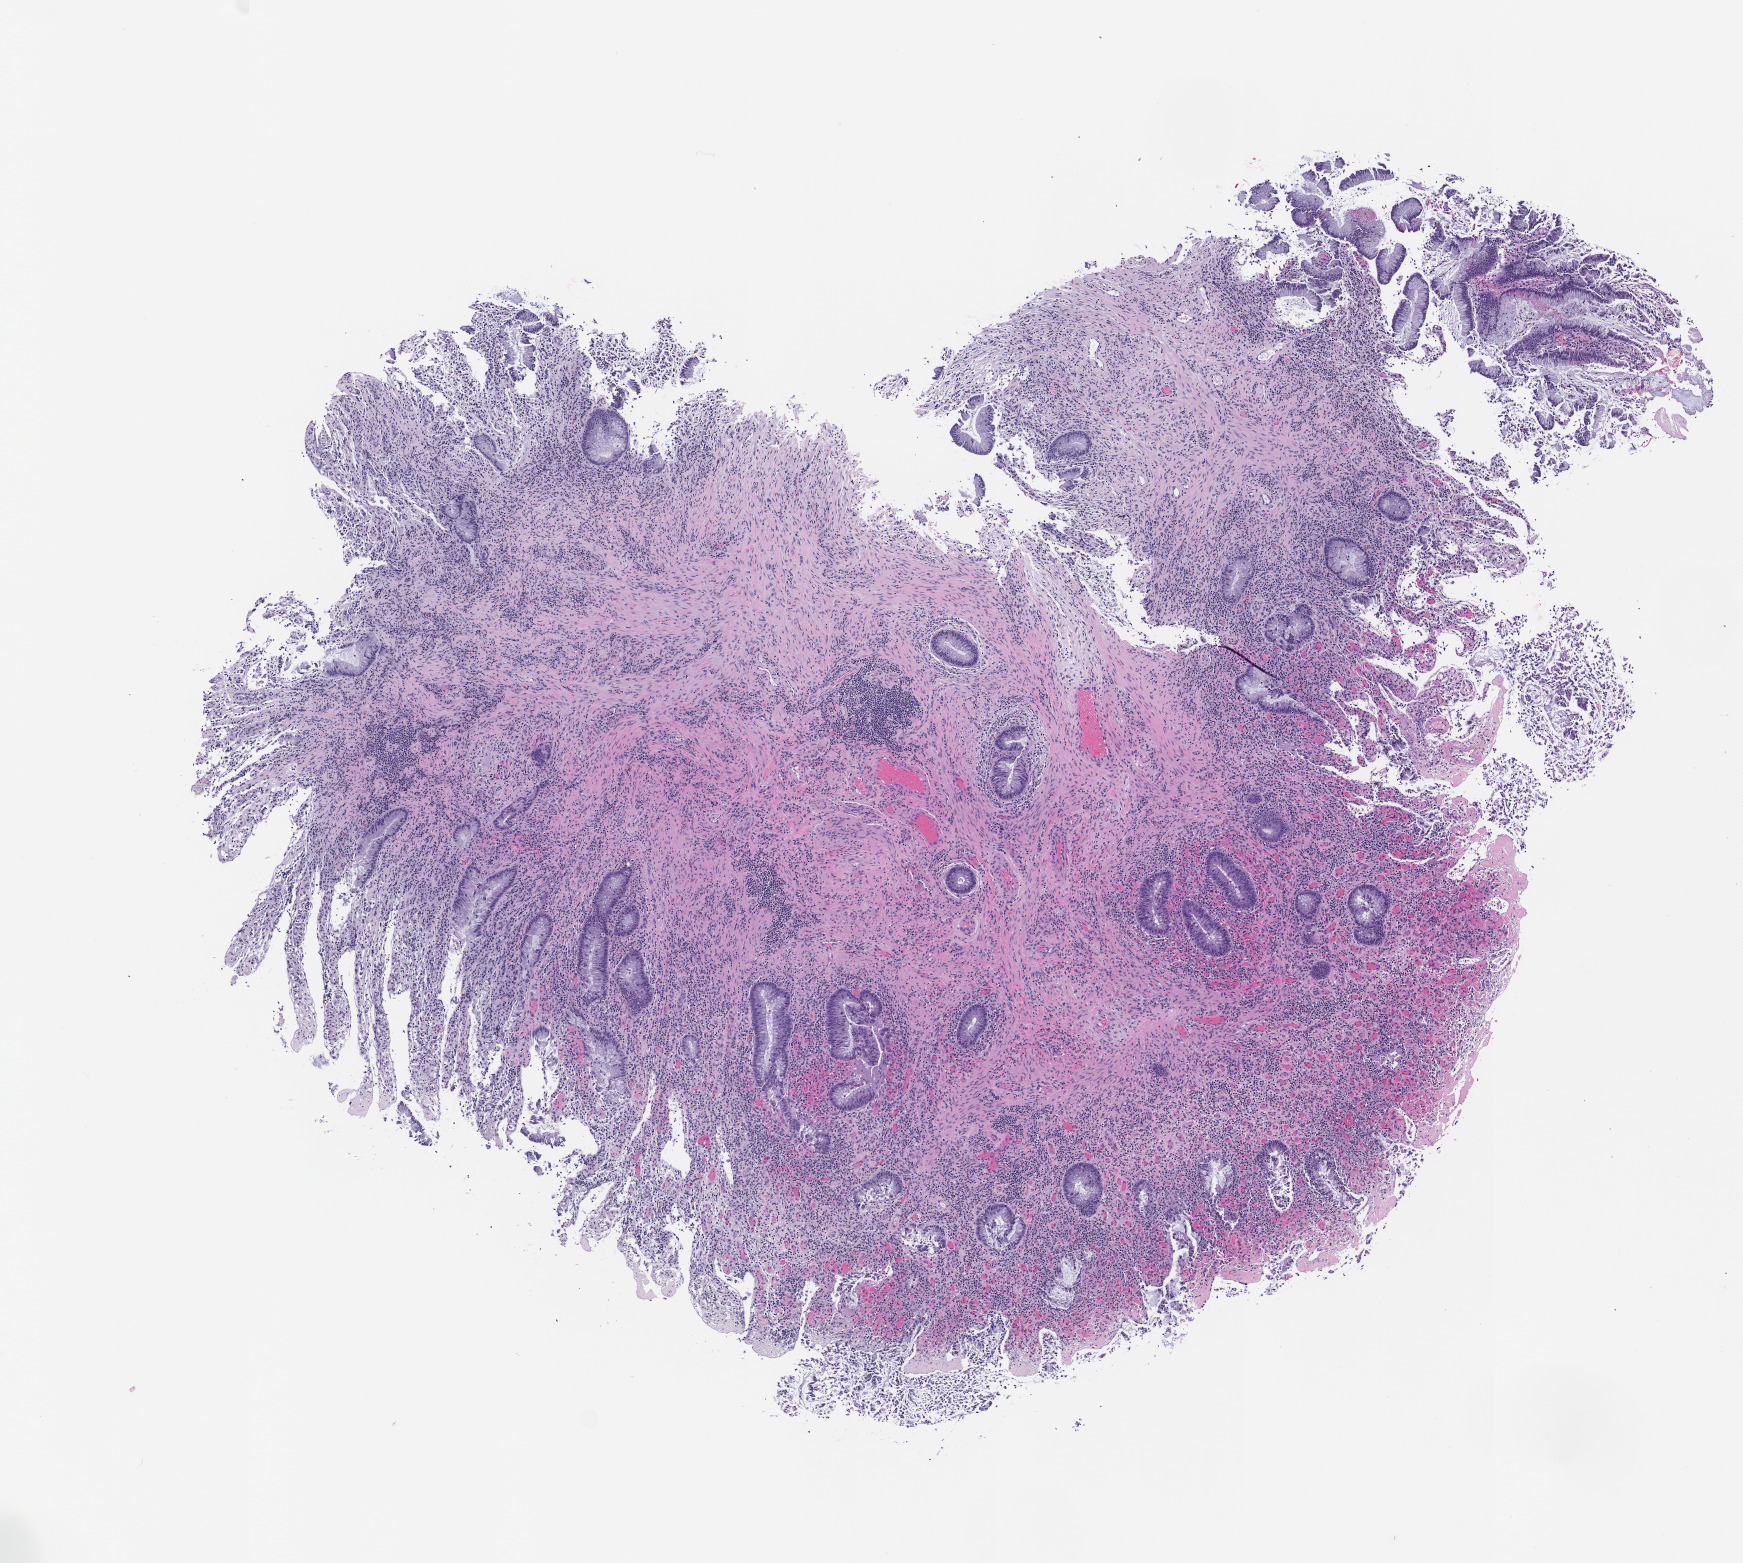
Digitized hematoxylin and eosin (H&E)-stained section of the patient's (originator) tumor tissue, shown as a low-resolution overview of the whole scanned area (about 7.0 x 6.3 mm), formalin-fixed paraffin-embedded section, originating tumor site category: colon. Patient sex: male.
Diagnosis: Colon Adenocarcinoma.